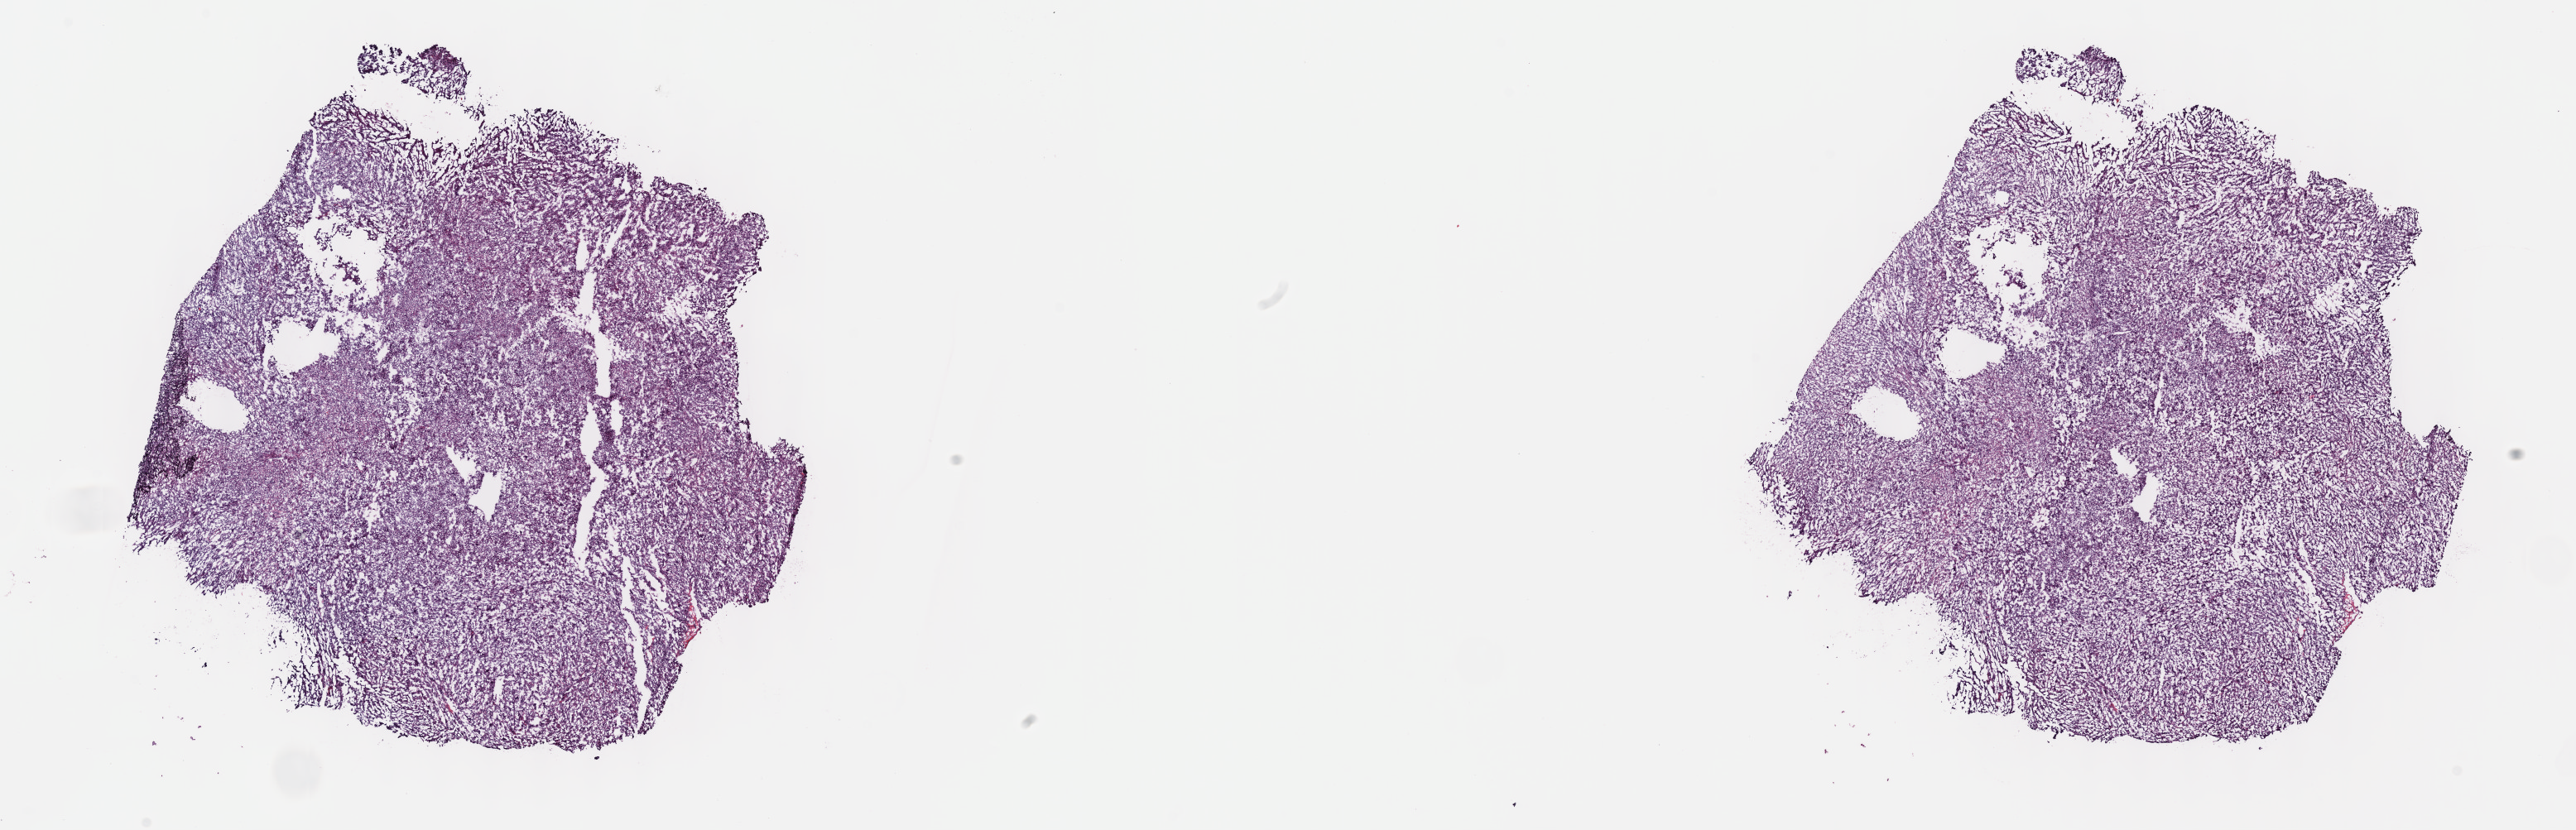
H&E whole-slide image — low-resolution overview of the scanned area, about 25.2 x 8.1 mm (acquisition: 40x scan), frozen section from the top of the tissue portion, primary tumour sample from the connective, subcutaneous and other soft tissues. Male, age 75 years at initial diagnosis. Composition of this section per pathologist review: tumour cells 90%, tumour nuclei 95%, normal cells 0%, stromal cells 5%, necrosis 5%. Inflammatory infiltration, as recorded: lymphocyte infiltration 0%, monocyte infiltration 0%, neutrophil infiltration 0%.
* pathologic diagnosis: Undifferentiated sarcoma